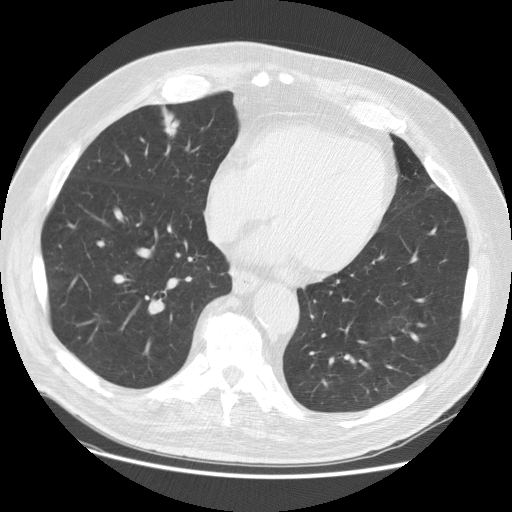
Low-dose screening chest CT, one axial slice; slice 42 of 129 in the series (ordered by position); reconstruction kernel STANDARD; lung window (W 1500 / L -600 HU); 2.5 mm slice thickness; 512 × 512 image matrix, field of view 397 × 397 mm.
Annotated regions visible in this slice (outlined manually by an expert reader):
- lesion 1 (tumor, upper lobe of right lung): bounding box (x1, y1, x2, y2) in pixels: (162, 104, 179, 137)